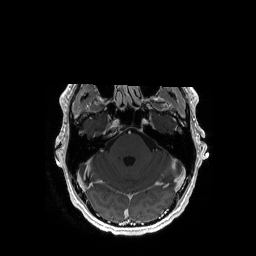
Brain MRI from a brain-tumour surgery series, one axial slice; position 125 of 192 along the scan axis; T1-weighted post-contrast; 1 mm slice thickness; 256 × 256 image matrix. Case-level facts recorded for this patient, not image findings: histopathology: Astrocytoma; WHO grade: 3; IDH mutation: yes.
Structures marked on this image (manually delineated by an expert):
- tumour: box from (x=157, y=124) to (x=165, y=134) px